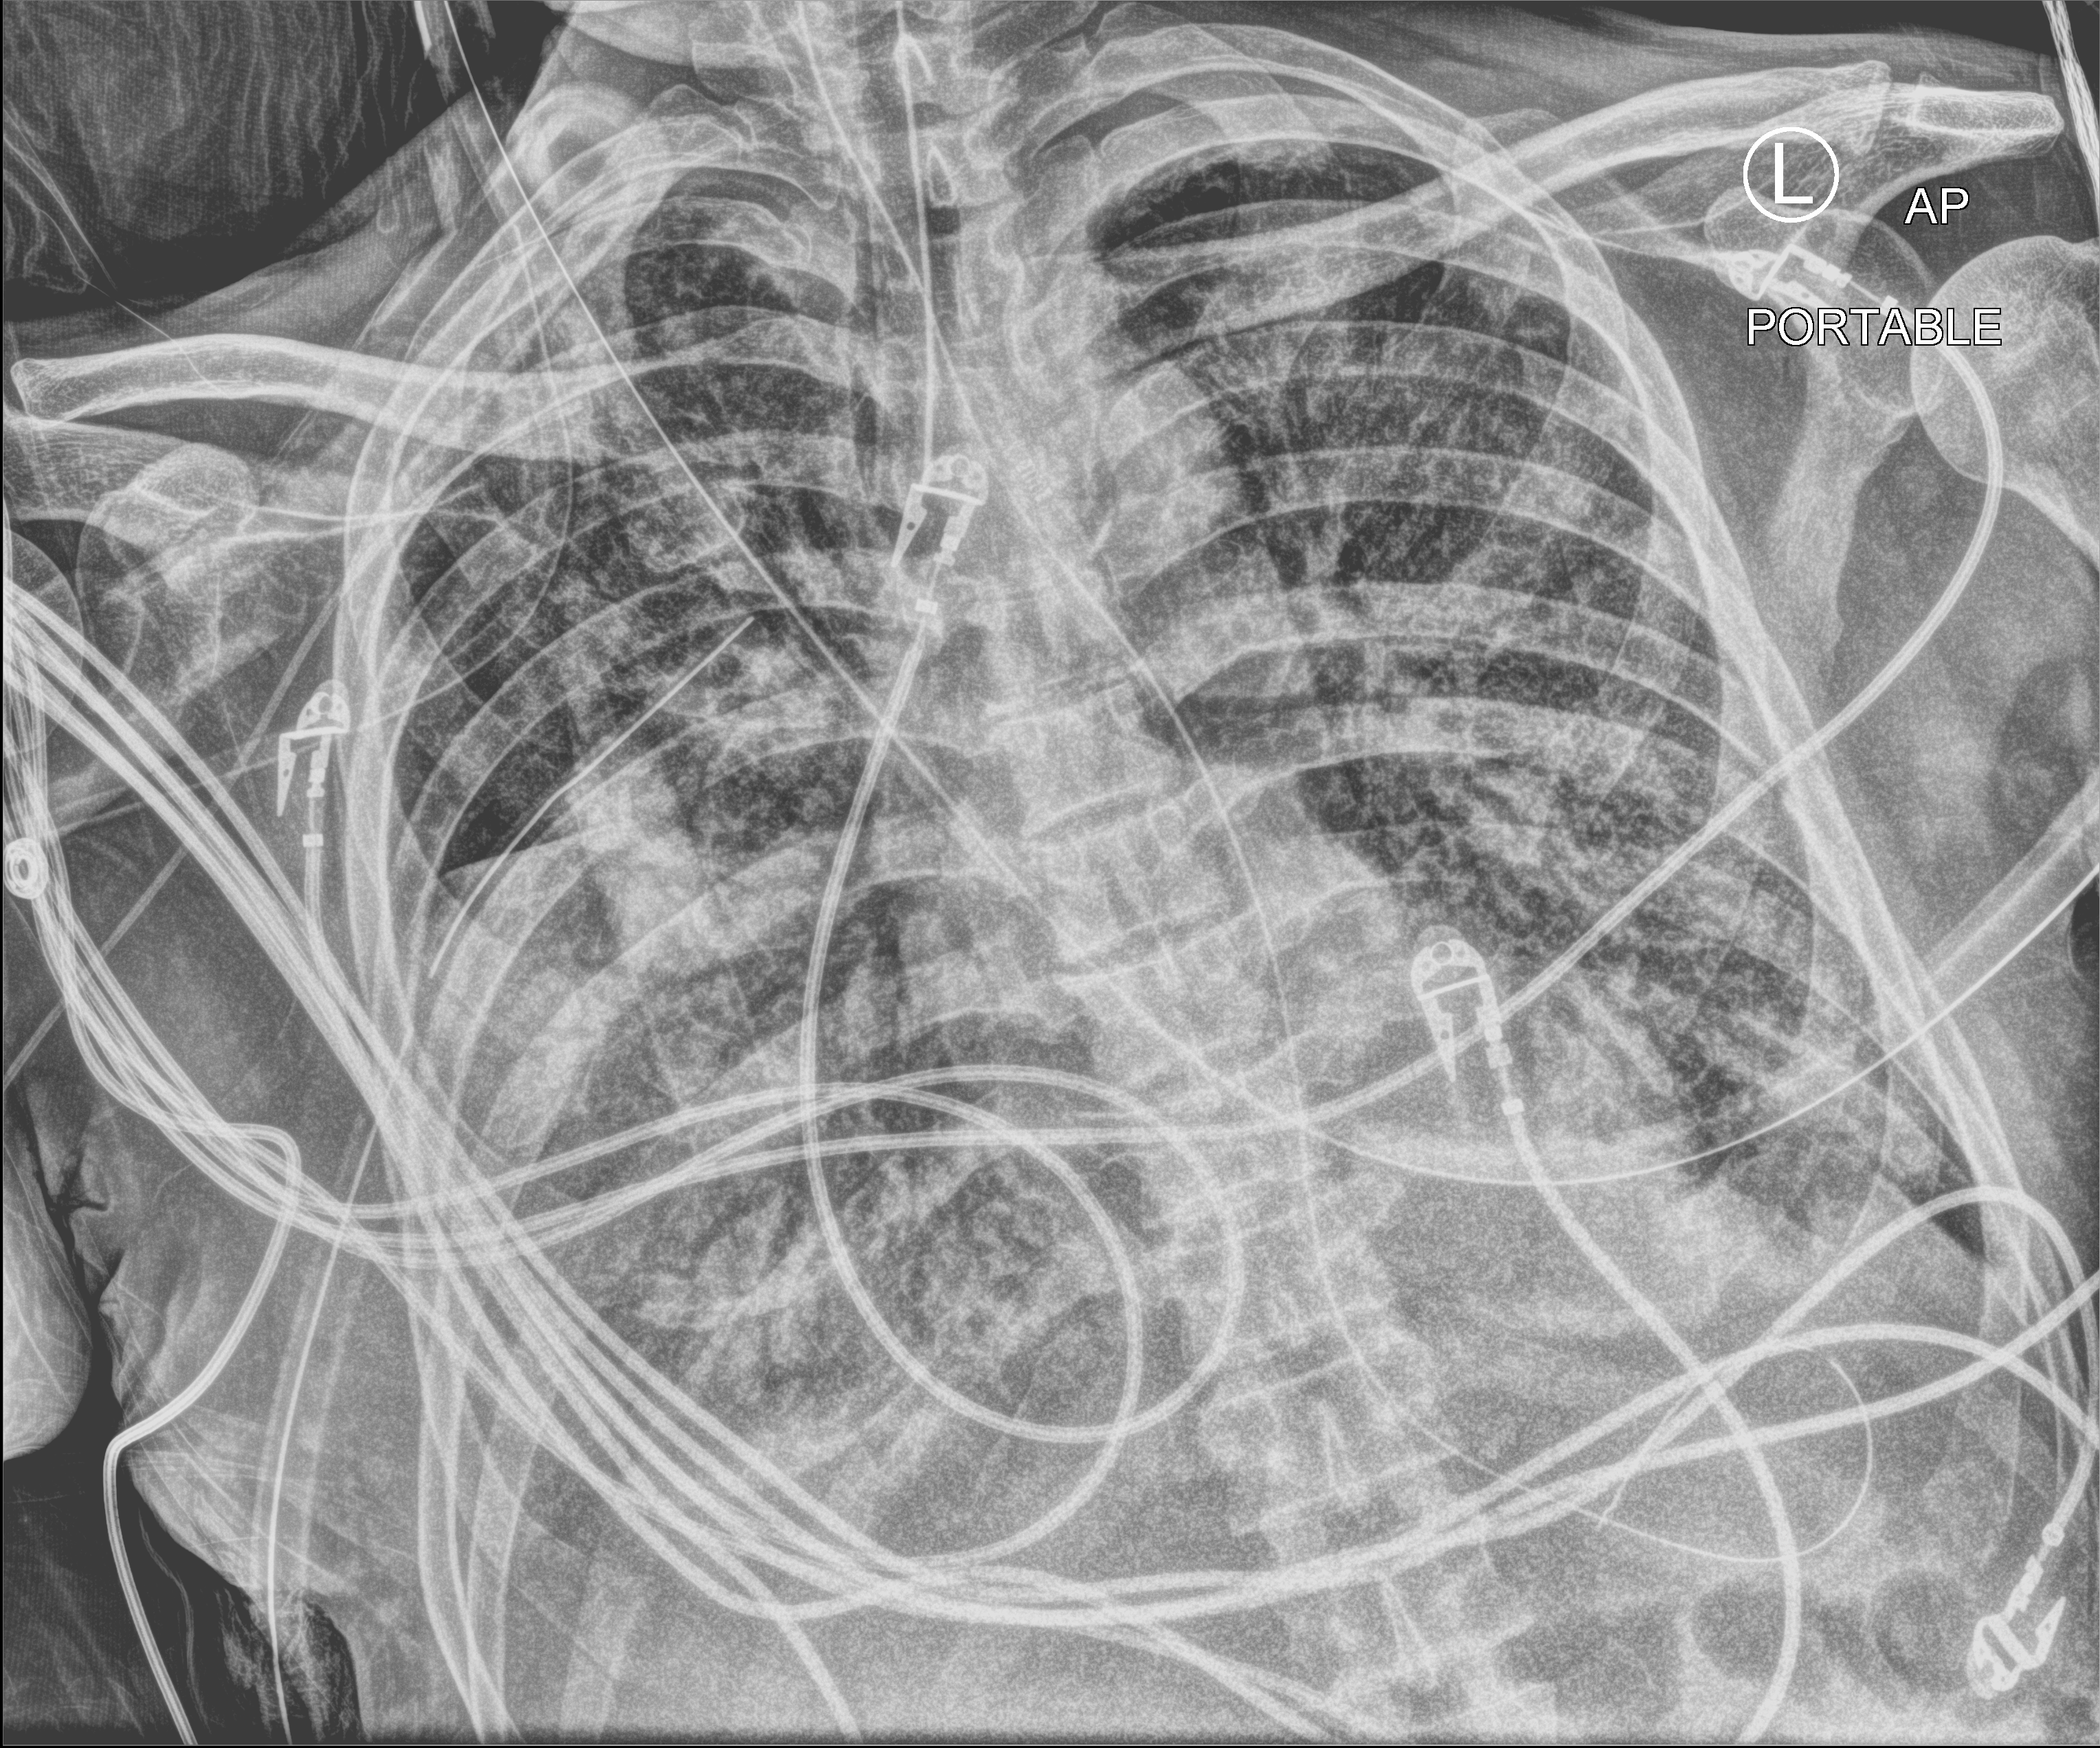
Bedside chest radiograph (computed radiography). Patient hospitalised with COVID-19; male, aged 60–74 years.
Hospital-stay facts (about this admission, not read from this image; timing relative to this image not recorded): admitted to intensive care during this hospital stay: yes; mechanically ventilated during this hospital stay: yes.